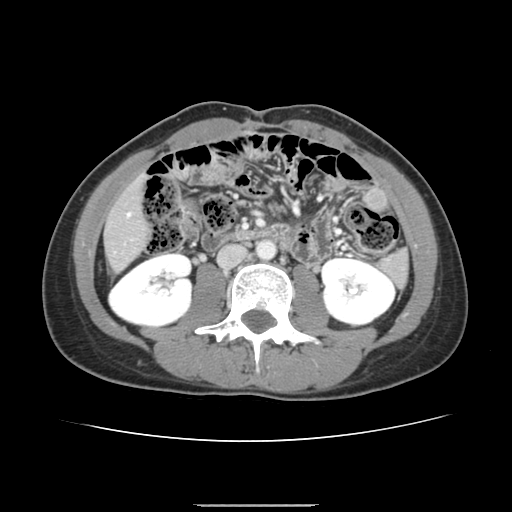
Contrast-enhanced abdominal CT, one axial slice. Slice 44 of 150 in the series (ordered by position). 120 kVp. Soft-tissue window (W 400 / L 40 HU). 512 × 512 image matrix. Female patient, age 32 years. From the clinical record (not read from this slice): diagnosis: colorectal cancer liver metastases, imaged before liver resection; multiple liver metastases: yes; largest metastasis: 0.7 cm.
Outlined on this slice (outlined manually by an expert reader):
- hepatic veins: bounding box <127,213,130,216> (left, top, right, bottom; pixels)
- liver: <106,183,148,270>
- planned liver remnant (the part of the liver to remain after resection): <106,183,148,270>